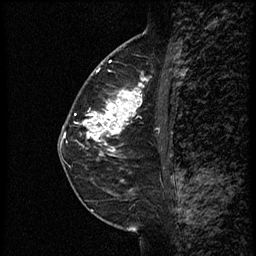
Breast MRI (dynamic contrast-enhanced), one sagittal slice. Position 31 of 60 along the scan axis. Dynamic contrast-enhanced study with each time point stored as its own series, time point 2 of 3 at this slice position (early post-contrast, ordered by acquisition time). 1.5 T. TE 4.2 ms, TR 18.9 ms. 256 × 256 image matrix, field of view 200 × 200 mm. Female patient. From the clinical record (not read from this slice): setting: breast cancer imaged before/during neoadjuvant chemotherapy; receptor status: HER2-positive.
Structures marked on this image (semi-automatic segmentation, software-assisted and operator-edited):
- analysis volume of interest (the breast-tissue region the enhancement analysis was run in; not a lesion): box from (x=77, y=65) to (x=161, y=147) px
- tumour enhancement mask (voxels above the 100 % enhancement threshold inside the analysis volume of interest): (x=85, y=74)–(x=150, y=147)